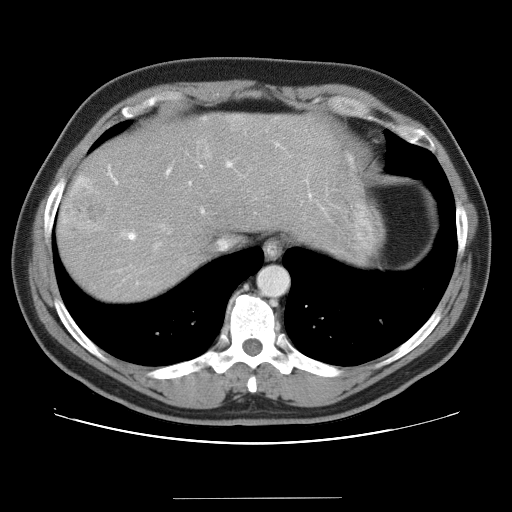
Contrast-enhanced abdominal CT (liver protocol), one axial slice. Slice 31 of 40 in the series (ordered by position). Soft-tissue window (W 400 / L 40 HU). 512 × 512 image matrix, field of view 380 × 380 mm. Case-level facts recorded for this patient, not image findings: diagnosis: hepatocellular carcinoma (patient treated with transarterial chemoembolisation; whether this scan precedes or follows treatment is not stated here); TNM stage (as recorded): Stage-IVA; Child-Pugh class: B.
Structures marked on this image (semi-automatic segmentation, software-assisted and operator-edited):
- abdominal aorta: bounding box (x1, y1, x2, y2) in pixels: (259, 266, 289, 296)
- liver parenchyma outside the tumour (the mass and vessels are separate outlines, so this box may not span the whole liver): (56, 112, 366, 300)
- mass: (58, 177, 115, 238)
- liver vessels: (108, 143, 323, 240)